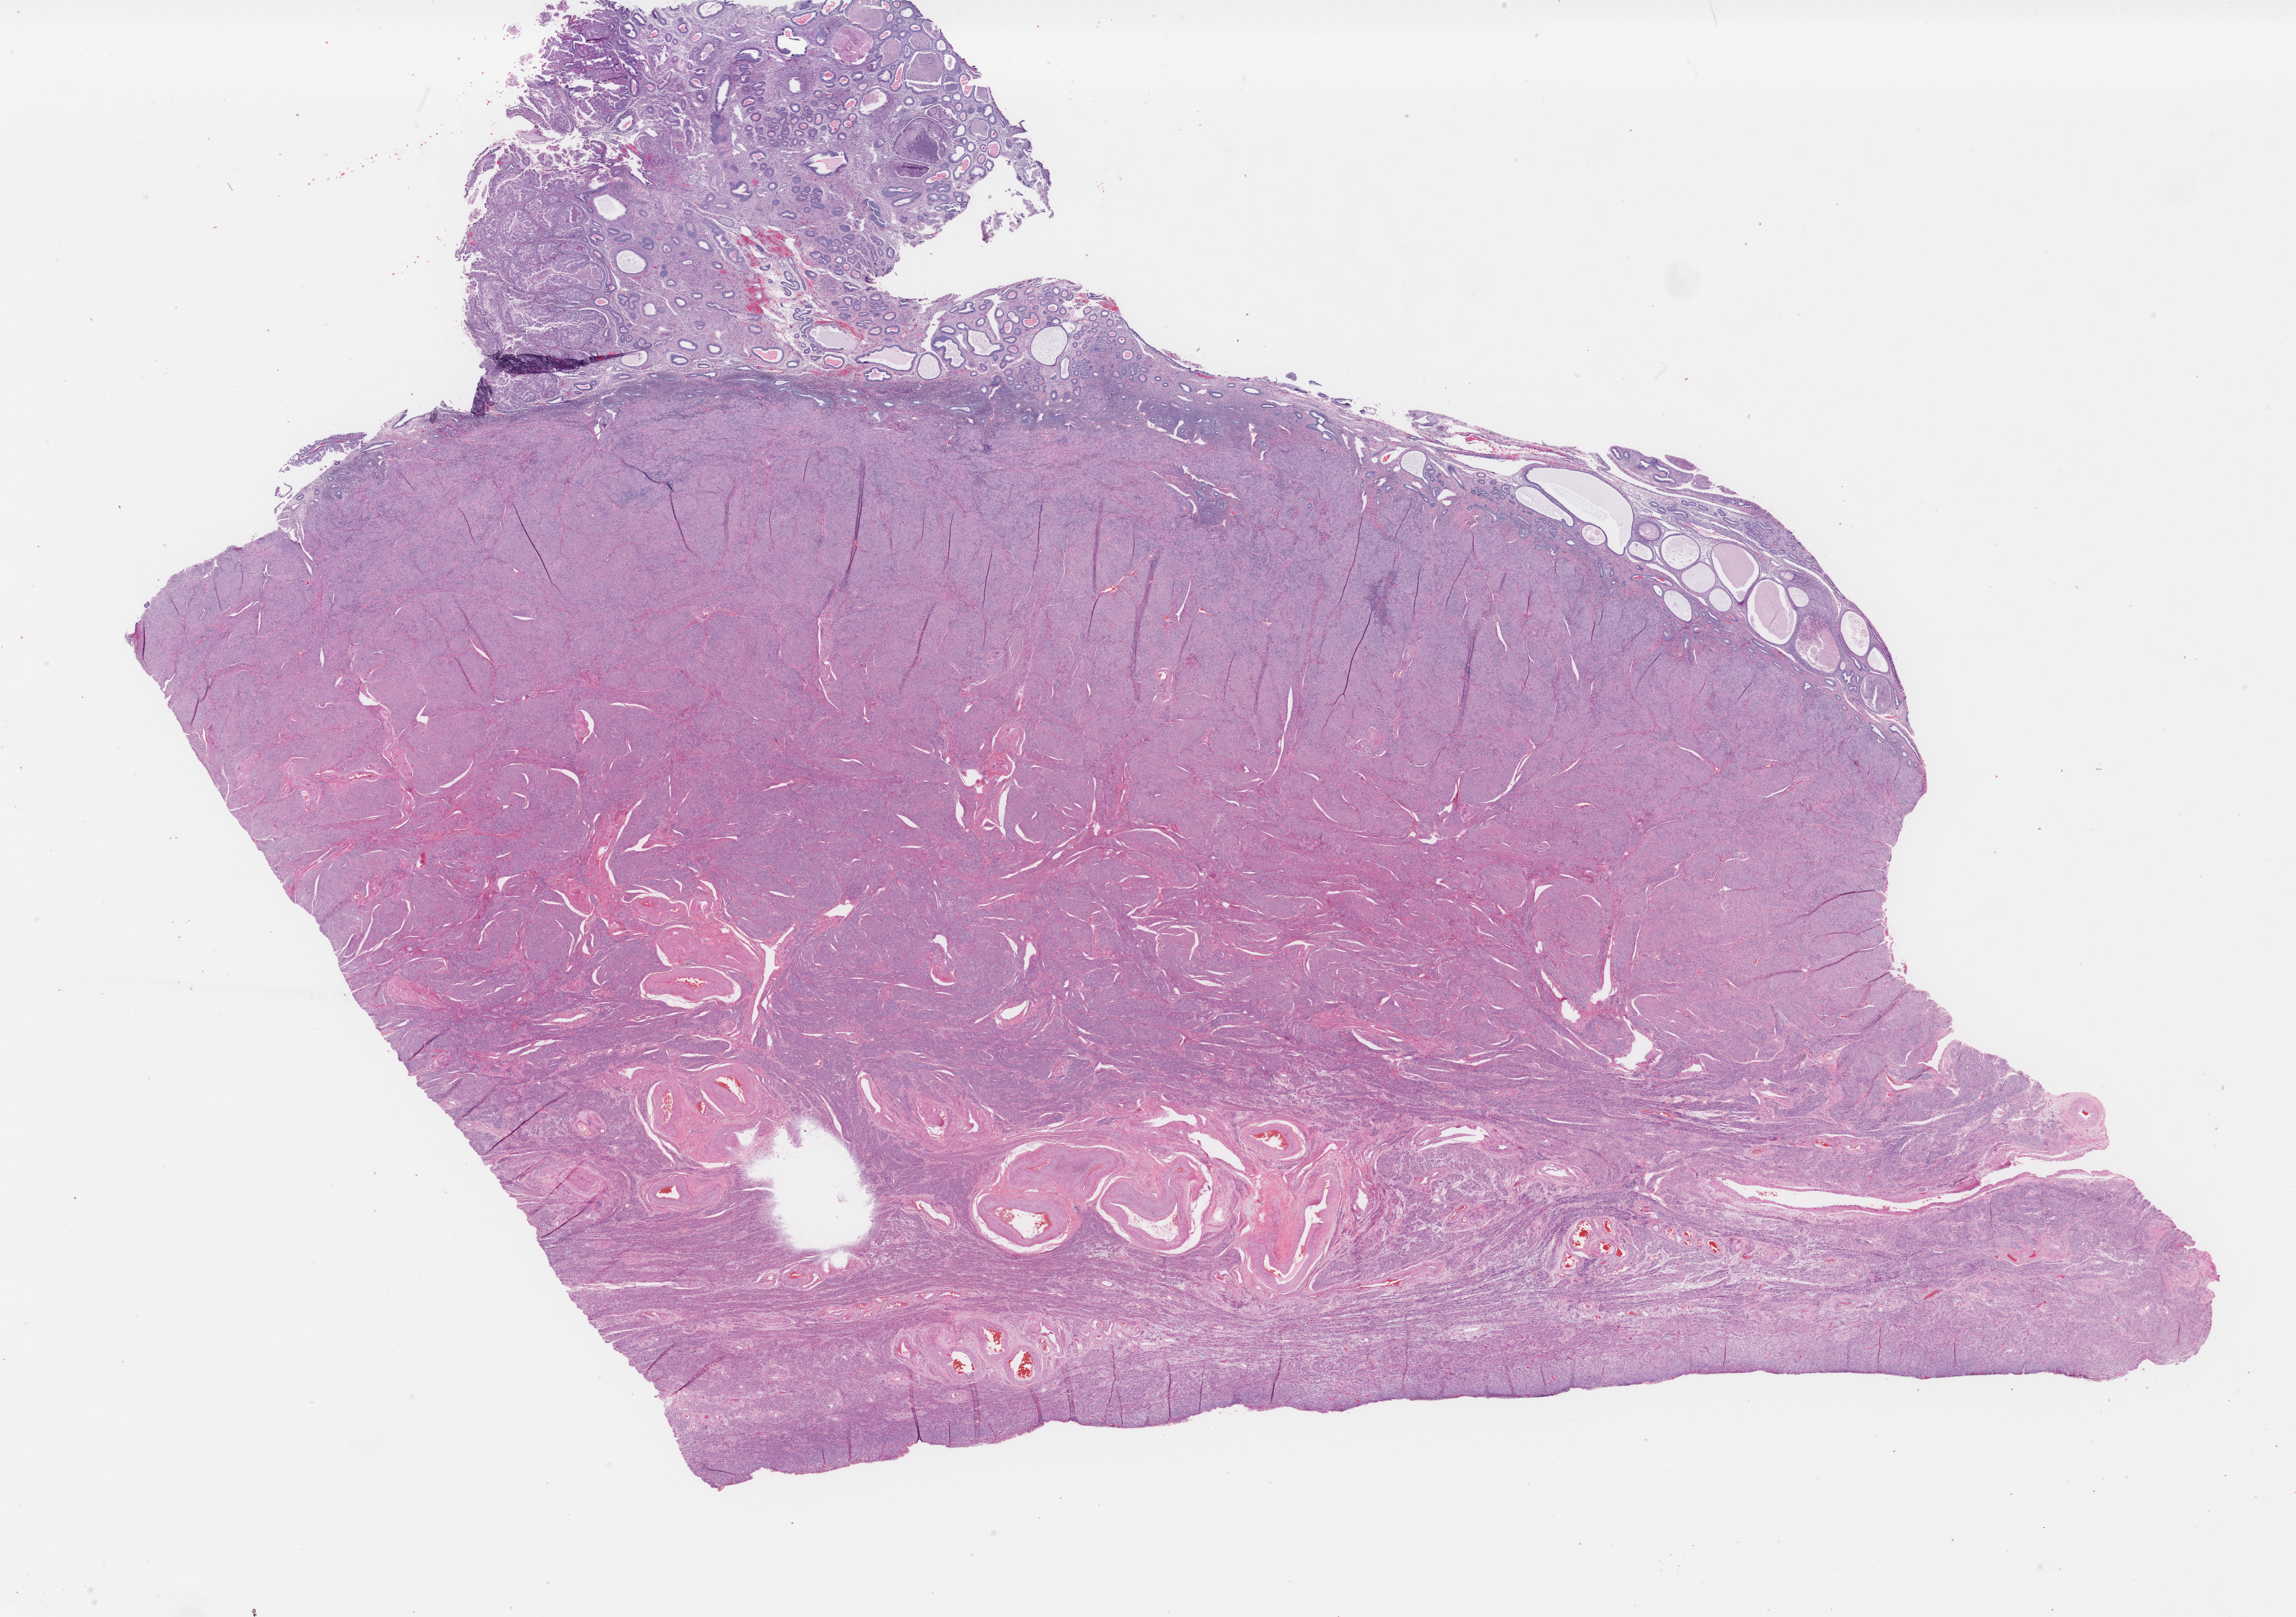
Hematoxylin and eosin (H&E) stained whole-slide image, low-resolution overview of the scanned area, about 30.7 x 21.6 mm, formalin-fixed paraffin-embedded (FFPE) diagnostic section, sample: primary tumour, uterus. Patient: female, age at initial diagnosis 62 years.
Pathologic diagnosis: Endometrioid adenocarcinoma, NOS (endometrium).